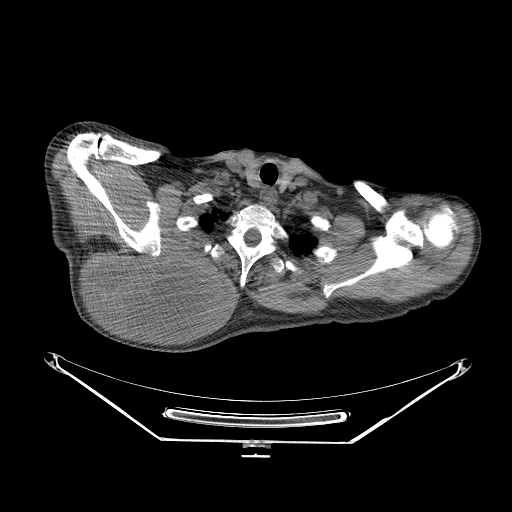
CT of an extremity soft-tissue mass (from a PET/CT study), one axial slice. Slice 206 of 267 in the series (ordered by position). 140 kVp. Soft-tissue window (W 400 / L 40 HU). 3.75 mm slice thickness. 512 × 512 image matrix. Male patient. From the clinical record (not read from this slice): histological type: pleiomorphic spindle cell undifferentiated; grade: high; site of the primary tumour: right parascapusular.
Annotated regions visible in this slice (expert contour drawn on MRI and transferred to this co-registered scan by the dataset authors):
- gross tumour volume including surrounding oedema: bounding box <85,242,234,328> (left, top, right, bottom; pixels)
- gross tumour volume (mass): <87,242,225,325>